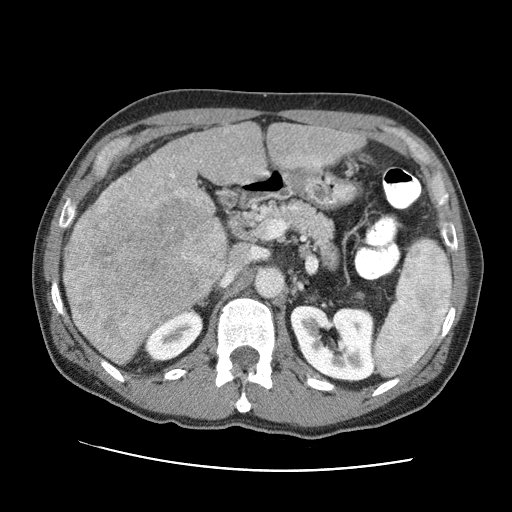
Contrast-enhanced abdominal CT (liver protocol), one axial slice. Slice 41 of 95 in the series (ordered by position). Reconstruction kernel STANDARD. 120 kVp. One of 2 acquisitions stored at this slice position. Soft-tissue window (W 400 / L 40 HU). 512 × 512 image matrix, field of view 360 × 360 mm. Case-level facts recorded for this patient, not image findings: diagnosis: hepatocellular carcinoma (patient treated with transarterial chemoembolisation; whether this scan precedes or follows treatment is not stated here); TNM stage (as recorded): Stage-IVA; Child-Pugh class: A; tumour differentiation: moderately differentiated; tumour nodularity: multinodular.
Outlined on this slice (semi-automatic segmentation, software-assisted and operator-edited):
- liver parenchyma outside the tumour (the mass and vessels are separate outlines, so this box may not span the whole liver): bounding box <110,122,364,224> (left, top, right, bottom; pixels)
- mass: <63,170,229,366>
- liver vessels: <129,130,330,183>